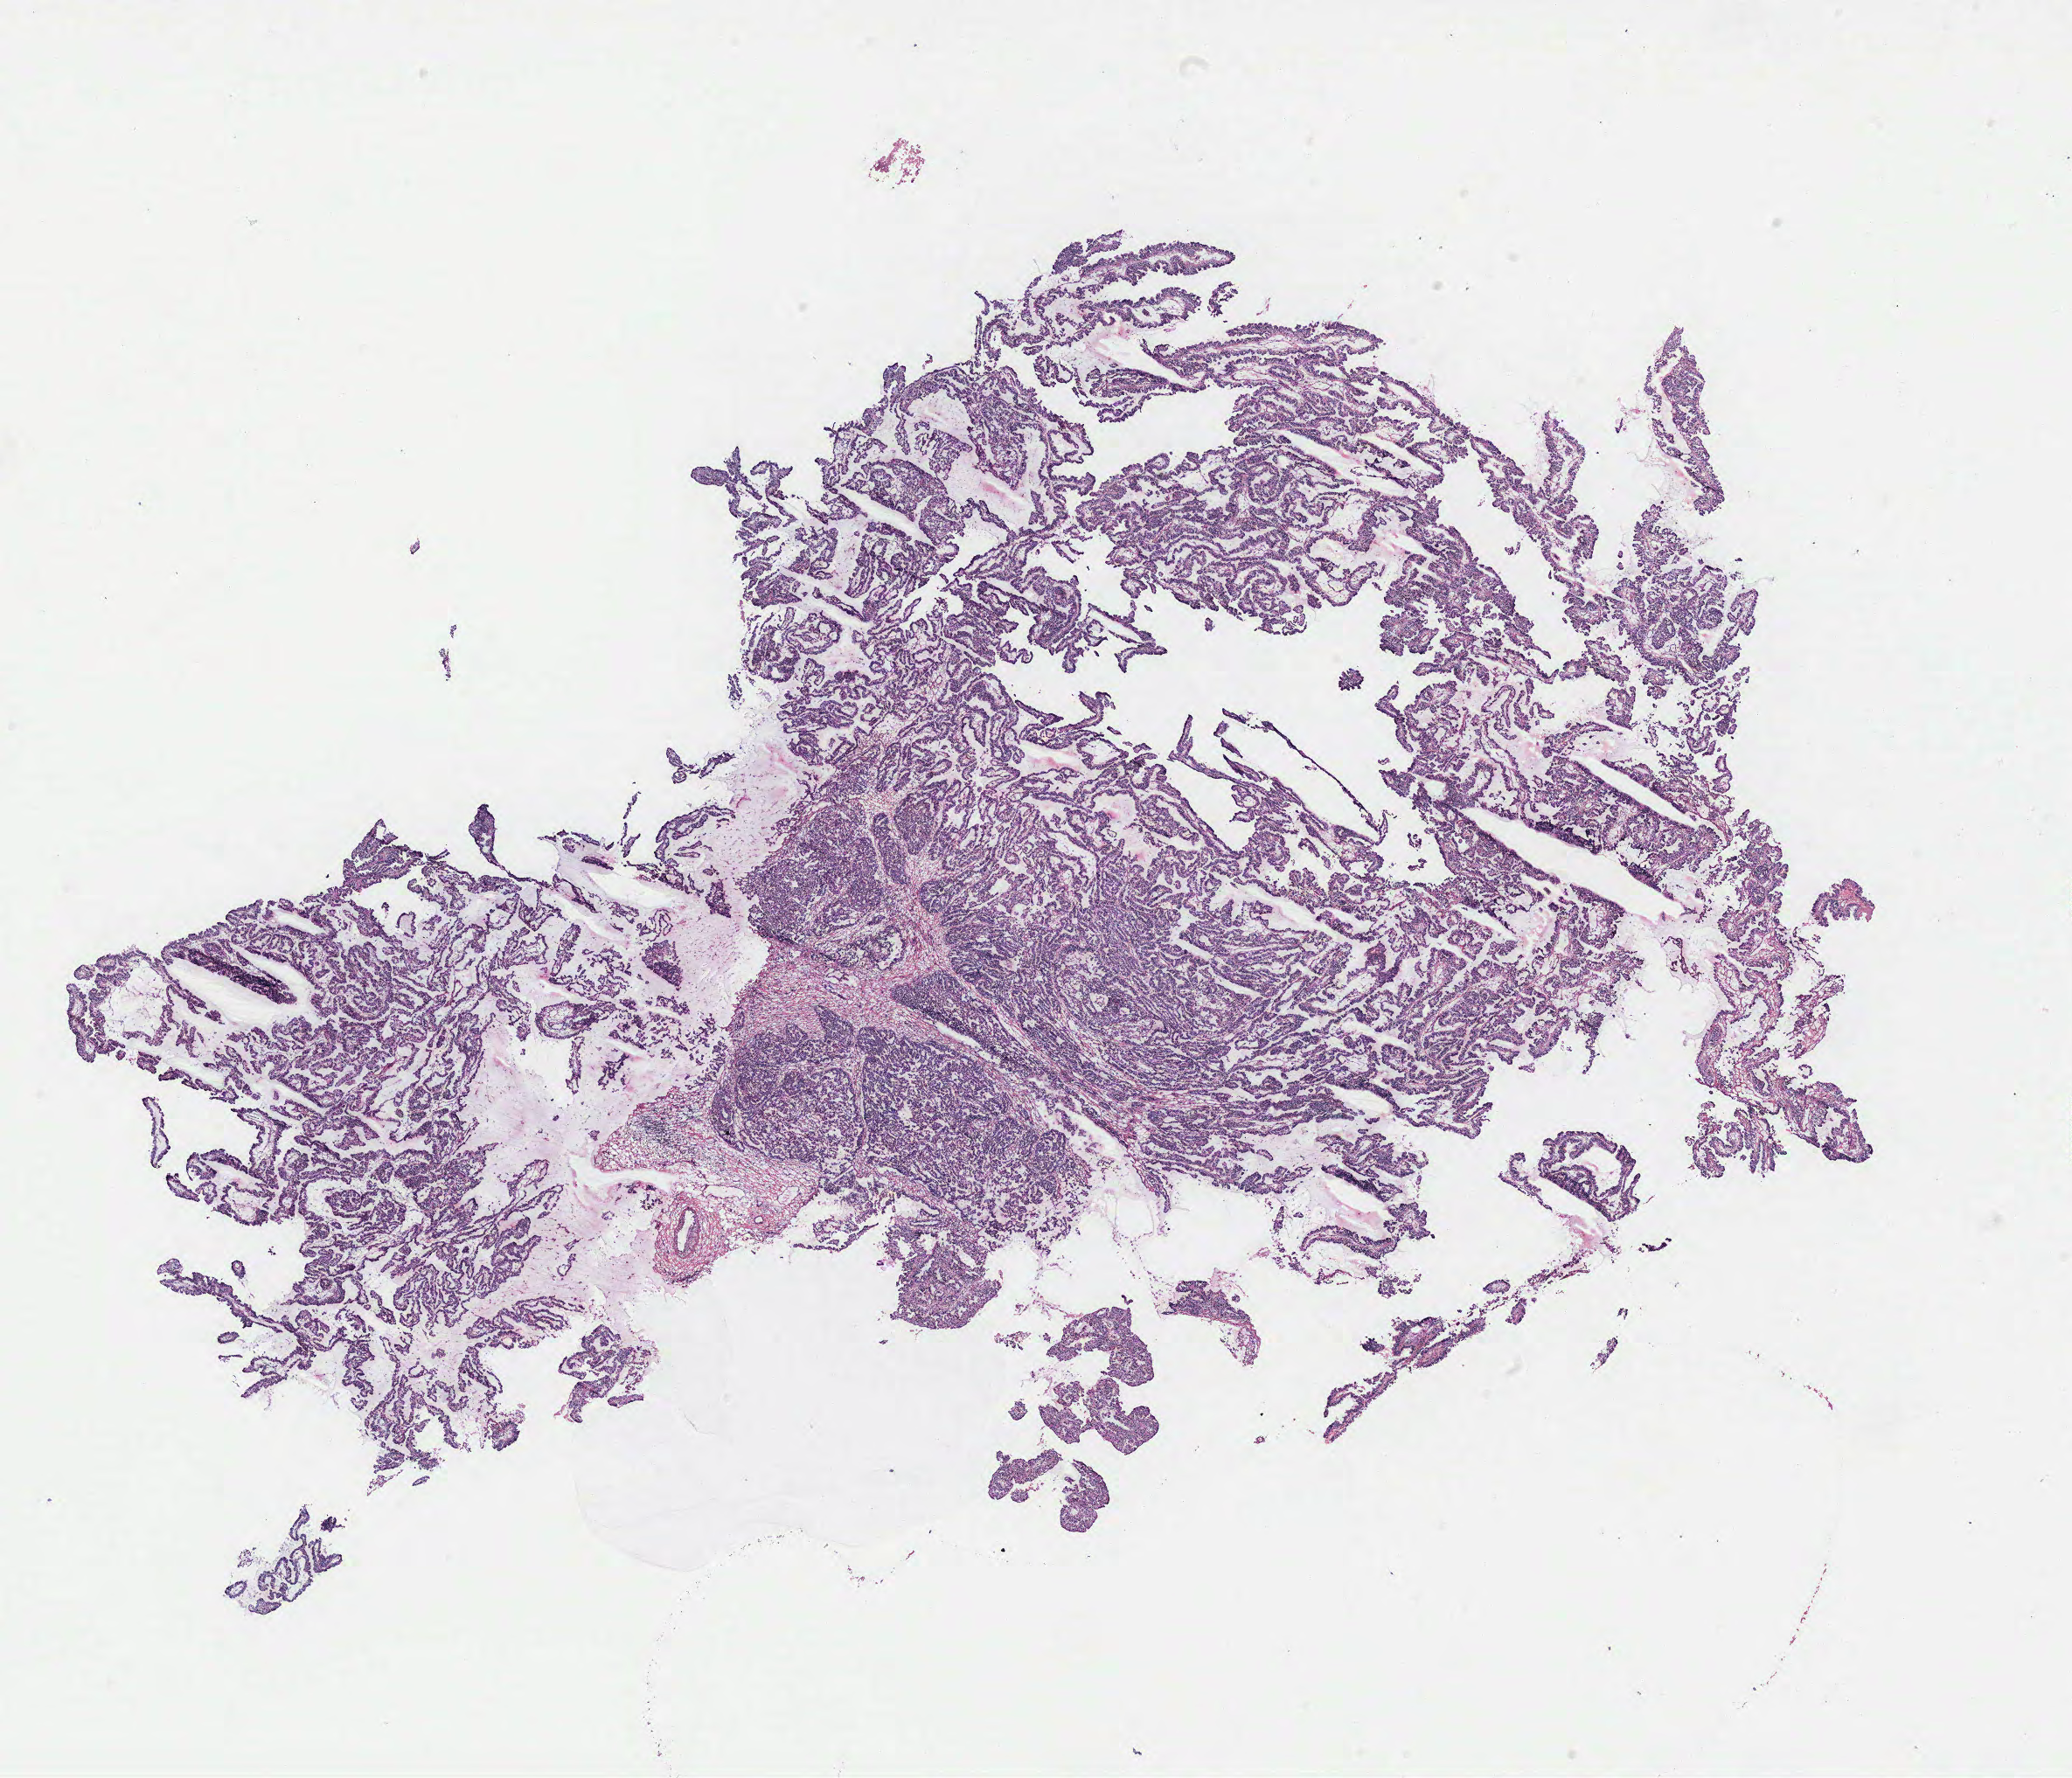
Whole-slide histology image, H&E-stained, whole scanned area (about 19.0 x 16.3 mm, slide scanned at 40x) shown as a low-resolution overview; ovary, normal (non-tumour) tissue. Patient: female, age 56 years.
- this section: normal (non-tumour) tissue from the same patient
- patient diagnosis: Serous adenocarcinoma, NOS